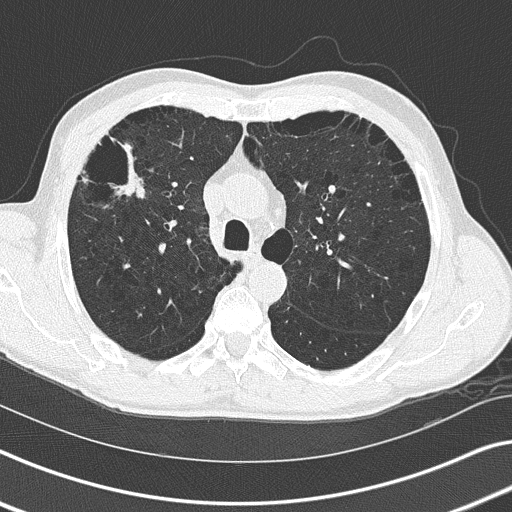
Axial slice from a low-dose chest CT screening exam. Third annual screen. Lung window (W 1500 / L -600 HU). 2 mm slice thickness. Lung (sharp) reconstruction kernel (B50f). Slice 58 of 170 in the series. Male, age 66 years at enrolment. Current smoker at enrolment.
- Expert reader's lesion annotation, bounding box [x1, y1, x2, y2] px = [85, 126, 162, 214].
- Screening reader's record for this exam (one nodule recorded; not confirmed to be the boxed lesion): non-calcified nodule or mass ≥4 mm, left lower lobe, 9 × 8 mm, smooth margins, soft tissue attenuation, pre-existing on the prior screen: yes; interval growth: no.
- Note: the box lies in the patient's right hemithorax on this image, whereas the reader's record names the left lung; they may be different findings.